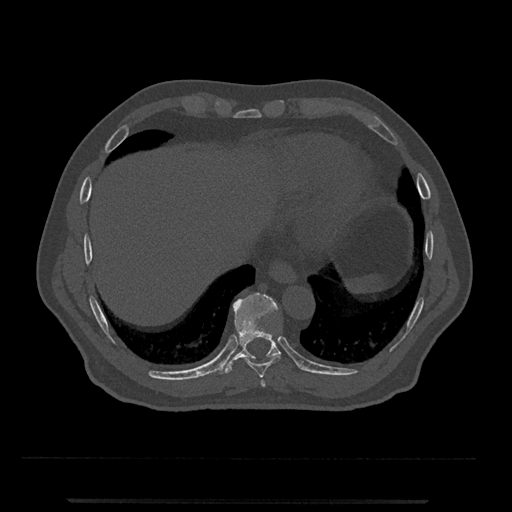
CT including the spine, one axial slice; position 546 of 797 along the scan axis; reconstruction kernel Br40s/3; bone window (W 1800 / L 400 HU); 512 × 512 image matrix. Patient: male, 63 years. Case-level facts recorded for this patient, not image findings: primary cancer: prostate.
Outlined on this slice (semi-automatically segmented with operator editing):
- T10 vertebra: bounding box (x1, y1, x2, y2) in pixels: (218, 293, 281, 374)
- T8 vertebra: (260, 380, 266, 387)
- T9 vertebra: (244, 354, 281, 378)